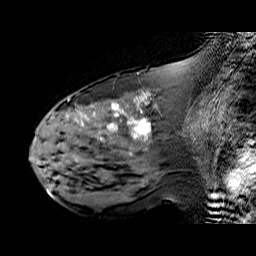
Breast MRI (dynamic contrast-enhanced), one sagittal slice; position 29 of 60 along the scan axis; dynamic contrast-enhanced series, time point 2 of 6 at this slice position (early post-contrast); 1.5 T; TE 6.3 ms, TR 32.9 ms; 4 mm slice thickness; 256 × 256 image matrix, field of view 200 × 200 mm. Female patient. From the clinical record (not read from this slice): setting: breast cancer imaged before/during neoadjuvant chemotherapy; receptor status: HER2-positive.
Annotated regions visible in this slice (semi-automatic segmentation, software-assisted and operator-edited):
- analysis volume of interest (the breast-tissue region the enhancement analysis was run in; not a lesion): bounding box [x1, y1, x2, y2] px = [48, 92, 195, 174]
- tumour enhancement mask (voxels above the 100 % enhancement threshold inside the analysis volume of interest): [66, 94, 146, 140]